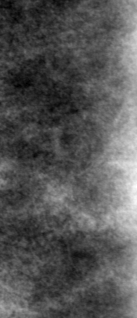
Cropped region of a digitized screen-film mammogram centred on a radiologist-marked abnormality, right breast, CC view, BI-RADS breast density category 2 (scale 1–4).
- Mass, shape oval, margins obscured; BI-RADS assessment category 0; subtlety rating 5 on a 1 (subtle) to 5 (obvious) scale; pathology result (as recorded, not read from the image): malignant.